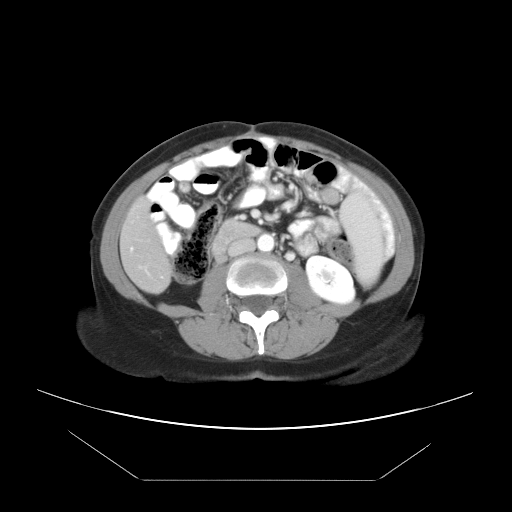
Contrast-enhanced abdominal CT, one axial slice. Slice 10 of 45 in the series (ordered by position). Reconstruction kernel STANDARD. 120 kVp. Intravenous contrast given. Soft-tissue window (W 400 / L 40 HU). 512 × 512 image matrix, field of view 405 × 405 mm. Female patient, age 52 years. Case-level facts recorded for this patient, not image findings: diagnosis: colorectal cancer liver metastases, imaged before liver resection; multiple liver metastases: yes.
Outlined on this slice (expert manual segmentation):
- hepatic veins: box from (x=131, y=248) to (x=133, y=250) px
- liver: (x=121, y=201)–(x=169, y=291)
- planned liver remnant (the part of the liver to remain after resection): (x=121, y=201)–(x=162, y=256)